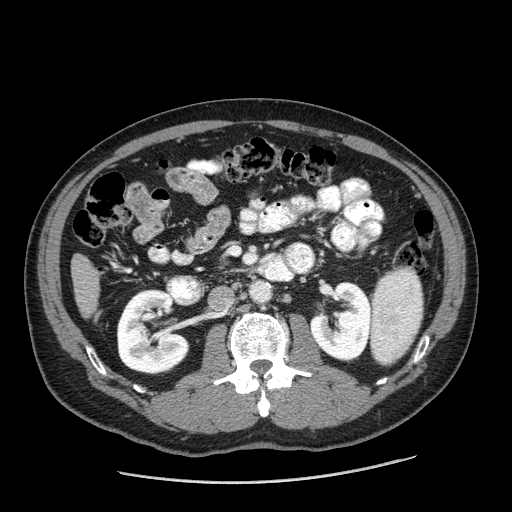
Contrast-enhanced abdominal CT (liver protocol), one axial slice; position 51 of 198 along the scan axis; 120 kVp; one of 2 acquisitions stored at this slice position; soft-tissue window (W 400 / L 40 HU); 2.5 mm slice thickness; 512 × 512 image matrix. From the clinical record (not read from this slice): diagnosis: hepatocellular carcinoma (patient treated with transarterial chemoembolisation; whether this scan precedes or follows treatment is not stated here); TNM stage (as recorded): Stage-II; Child-Pugh class: A; tumour differentiation: moderately differentiated; tumour nodularity: multinodular.
Annotated regions visible in this slice (semi-automatically segmented with operator editing):
- liver parenchyma outside the tumour (the mass and vessels are separate outlines, so this box may not span the whole liver): box from (x=70, y=254) to (x=100, y=317) px